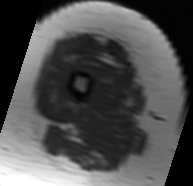
MRI of an extremity soft-tissue mass, one axial slice; slice 15 of 91 in the series (ordered by position); MR volume resampled by the dataset authors to the PET/CT grid (not the native acquisition matrix); 3.27 mm slice thickness; 193 × 186 image matrix. Female patient. From the clinical record (not read from this slice): histological type: malignant solitary fibrous tumor; grade: intermediate; site of the primary tumour: right thigh.
Structures marked on this image (expert contour drawn on MRI and transferred to this co-registered scan by the dataset authors):
- gross tumour volume including surrounding oedema: bounding box <72,37,125,75> (left, top, right, bottom; pixels)